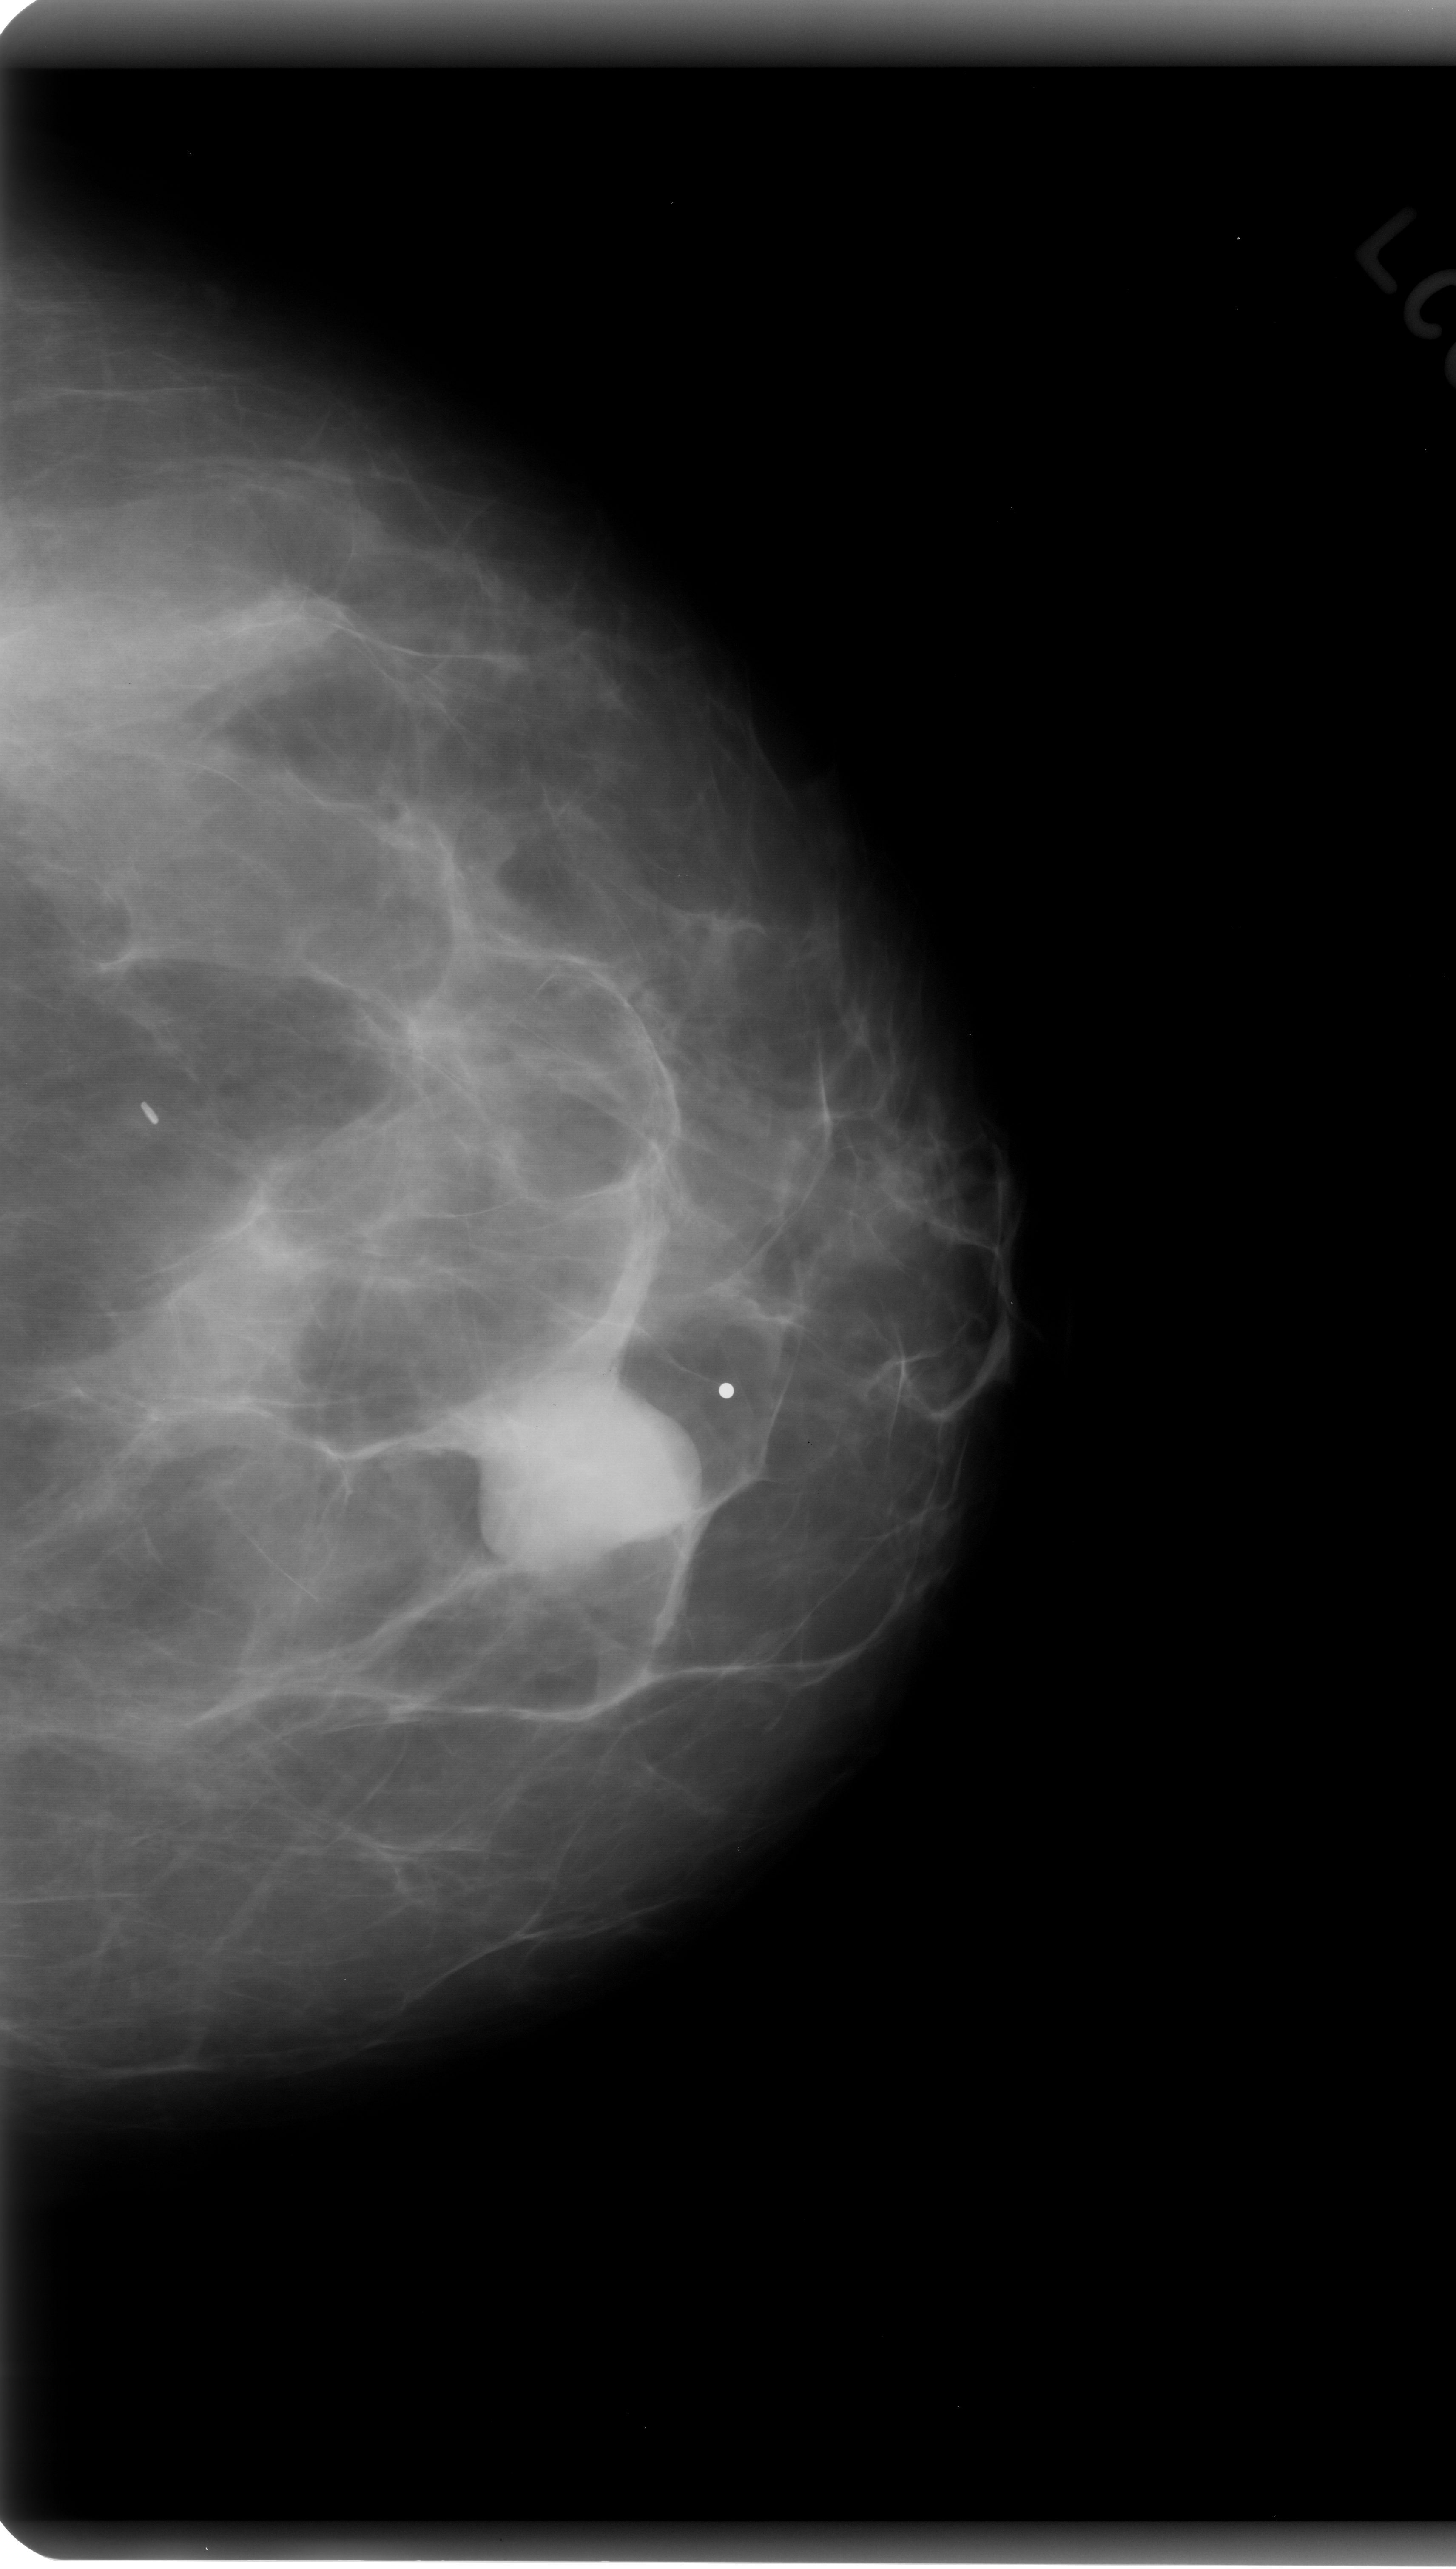
Digitized screen-film mammogram. Left breast. CC view. 1456 × 2569 image matrix.
Expert-marked regions of interest on this image (one box per marked abnormality):
- mass, shape oval, margins circumscribed; BI-RADS assessment category 4; pathology (as recorded): benign: bounding box <445,1348,705,1578> (left, top, right, bottom; pixels)